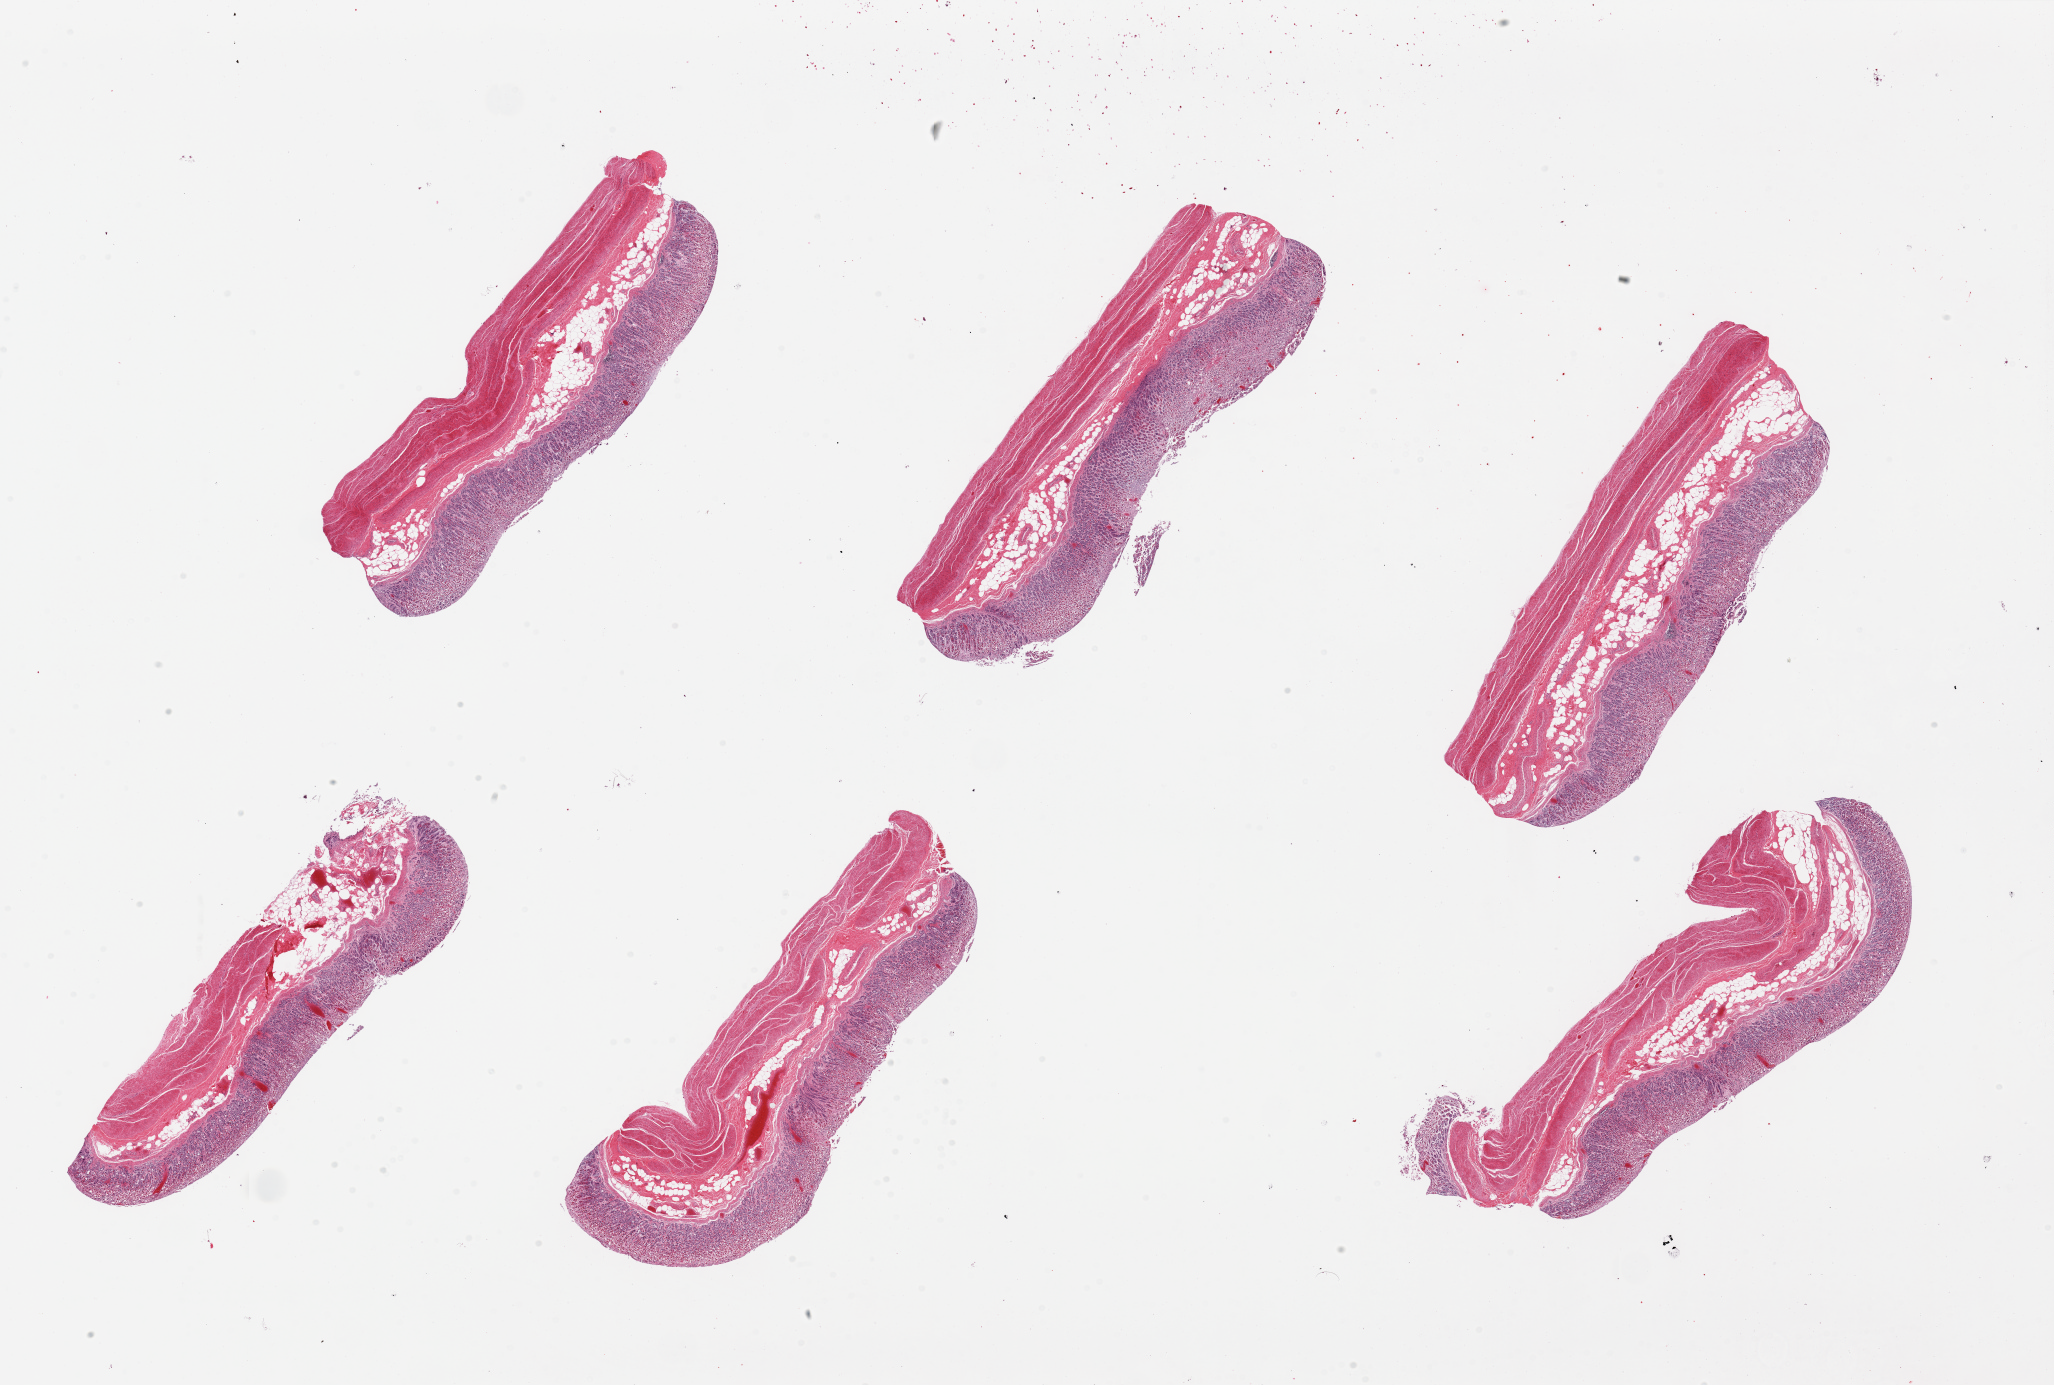
Whole-slide image, hematoxylin and eosin (H&E) stain — low-resolution overview of the scanned area, about 32.5 x 21.9 mm (slide scanned at 20x), PAXgene-fixed paraffin-embedded (PFPE) section, section of stomach (target tissue), donor tissue sample. Male donor.
Pathologist's review note for this sample: 6 pieces.